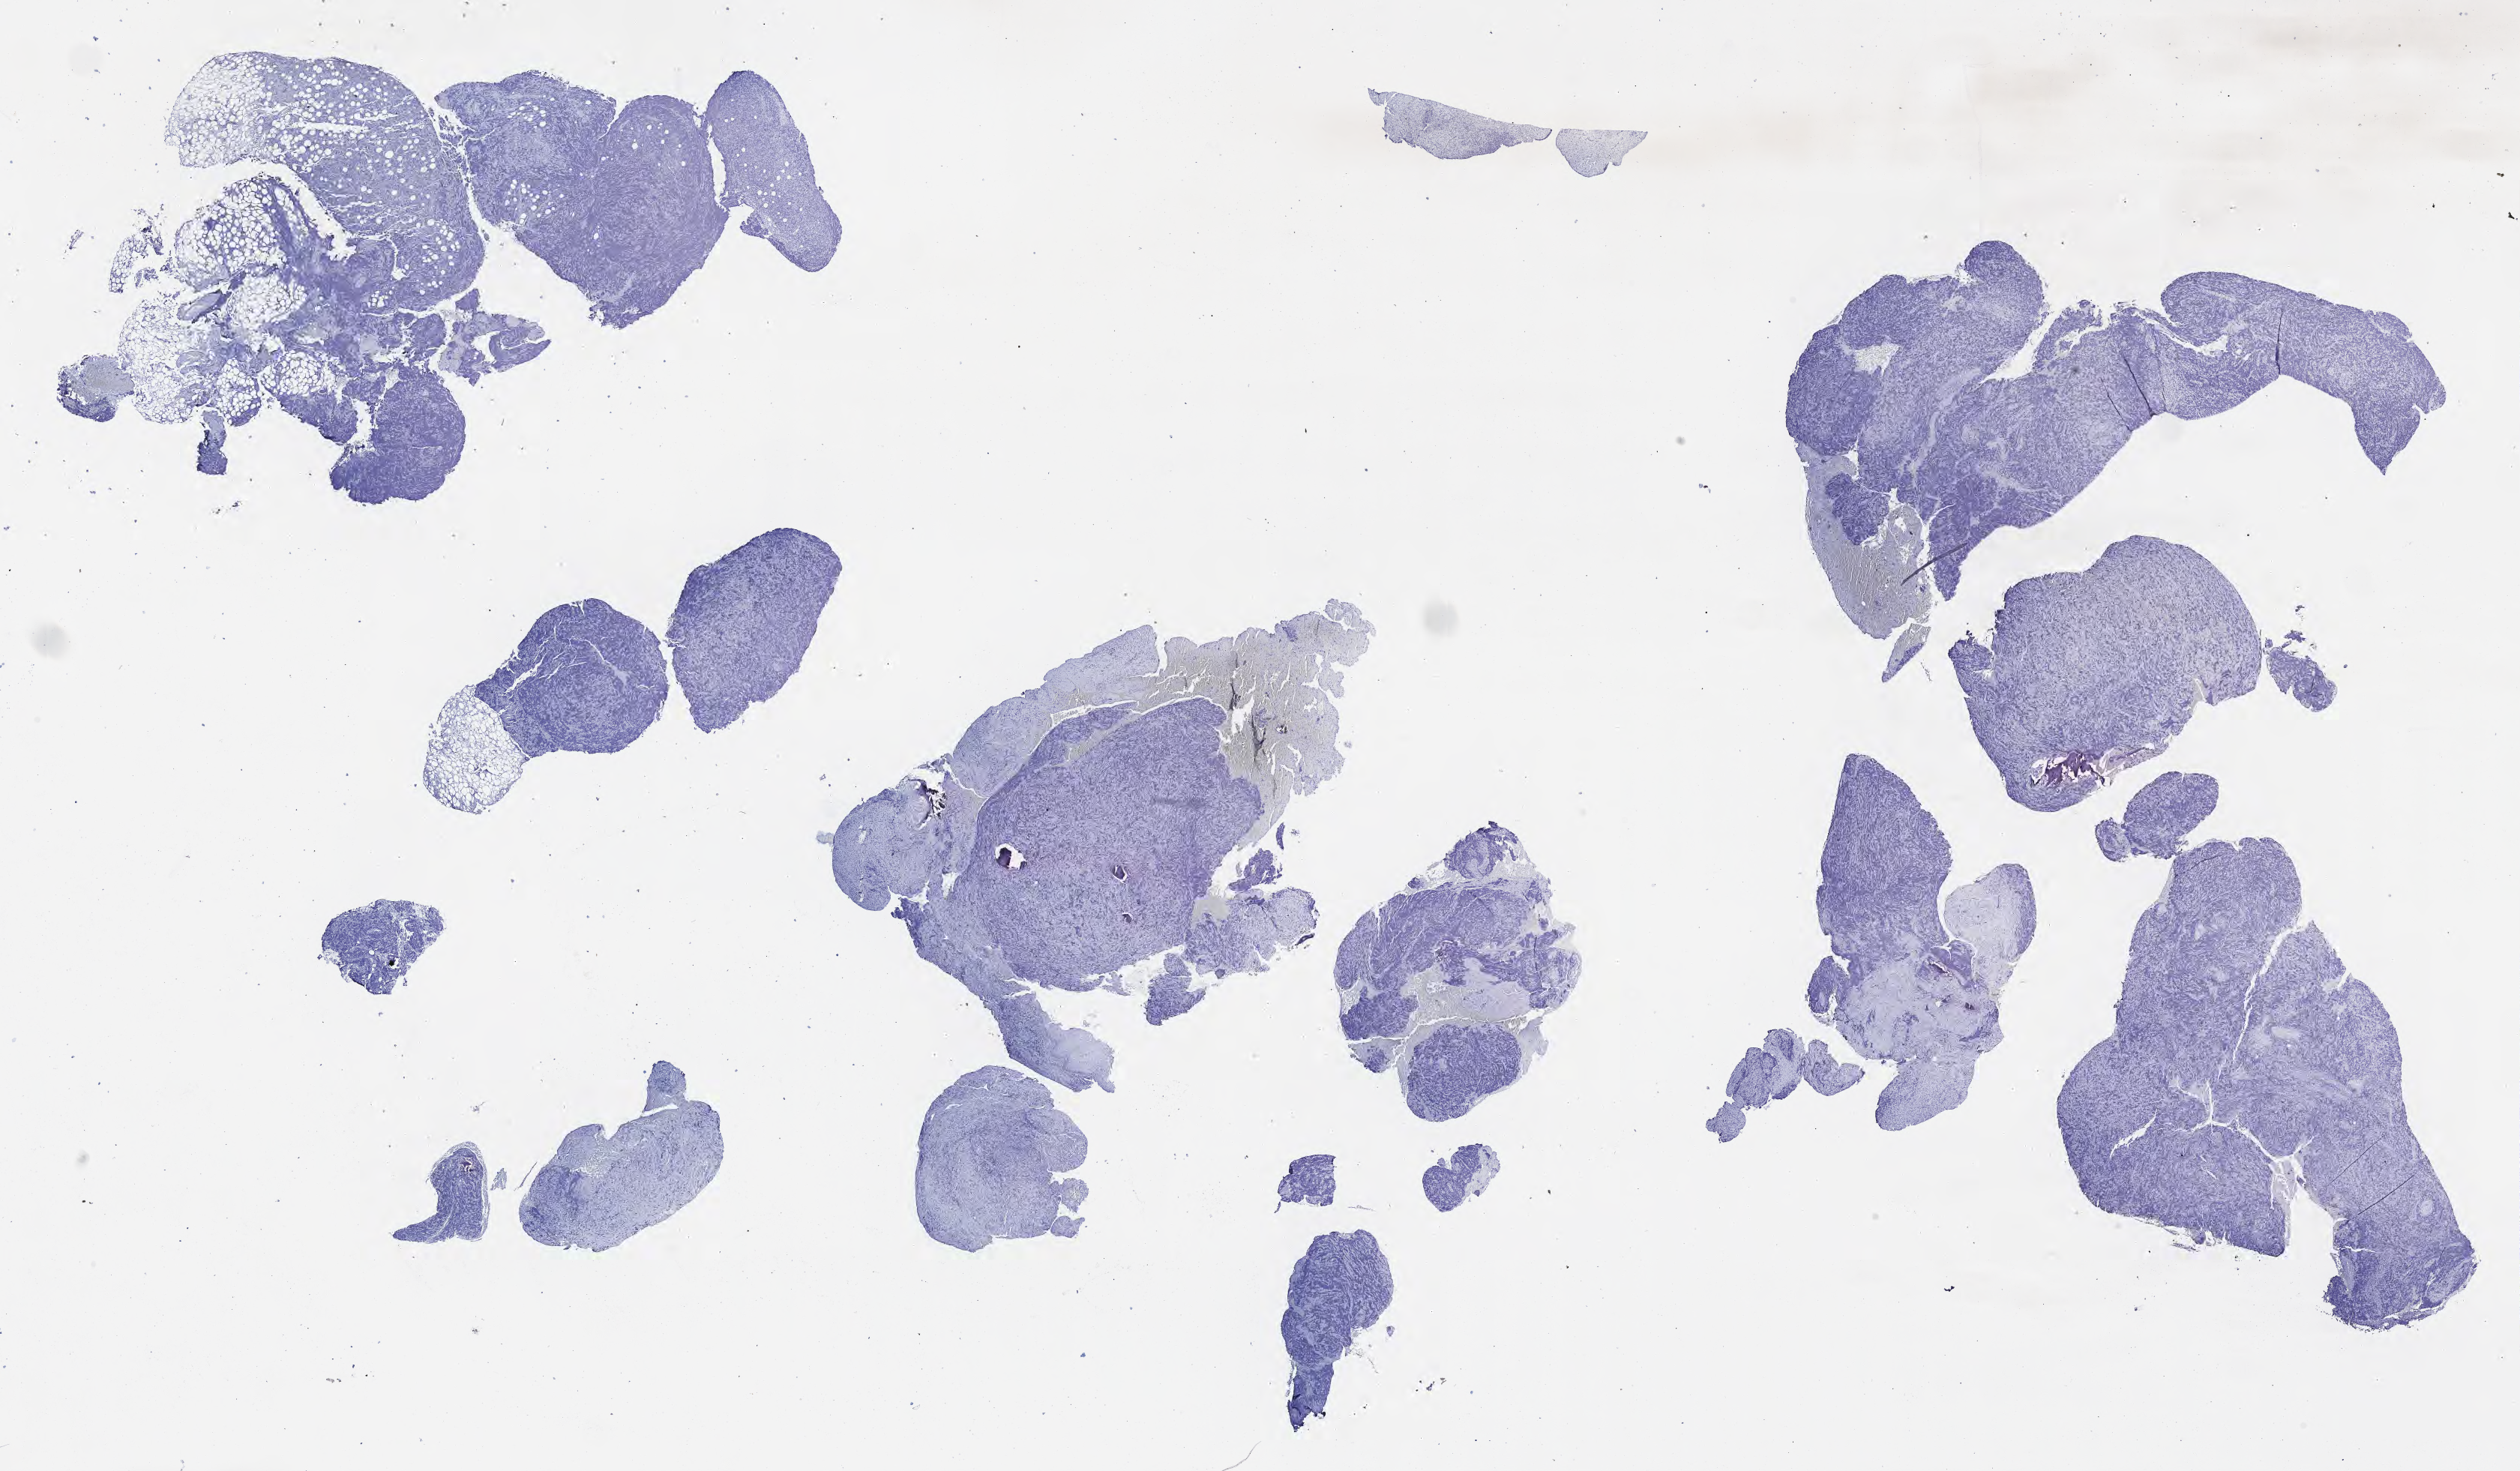
Immunohistochemistry (IHC) whole-slide image stained for p53 — low-resolution overview of the scanned area, about 27.2 x 15.9 mm, tumor tissue. Male patient, aged 45.
- diagnosis: Diffuse large B-cell lymphoma, NOS